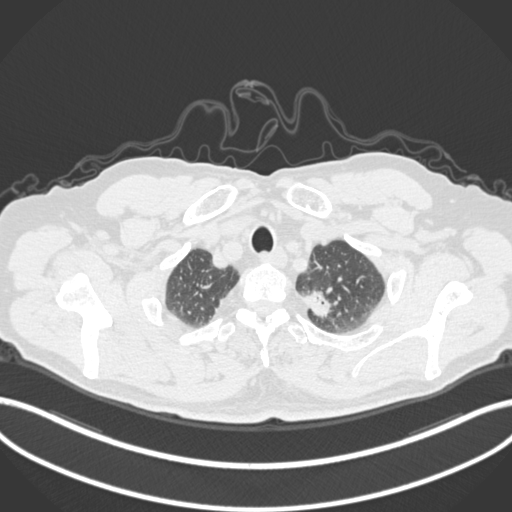
Chest CT, one axial slice. Slice 287 of 306 in the series (ordered by position). Lung window (W 1500 / L -600 HU). 512 × 512 image matrix, field of view 400 × 400 mm. Male patient, age 64 years. Case-level facts recorded for this patient, not image findings: clinical TNM (as recorded): T1c N0 M0.
Structures marked on this image (rectangle marked by the reading radiologist):
- lung tumour (recorded histology: adenocarcinoma): bounding box (x1, y1, x2, y2) in pixels: (301, 288, 334, 326)